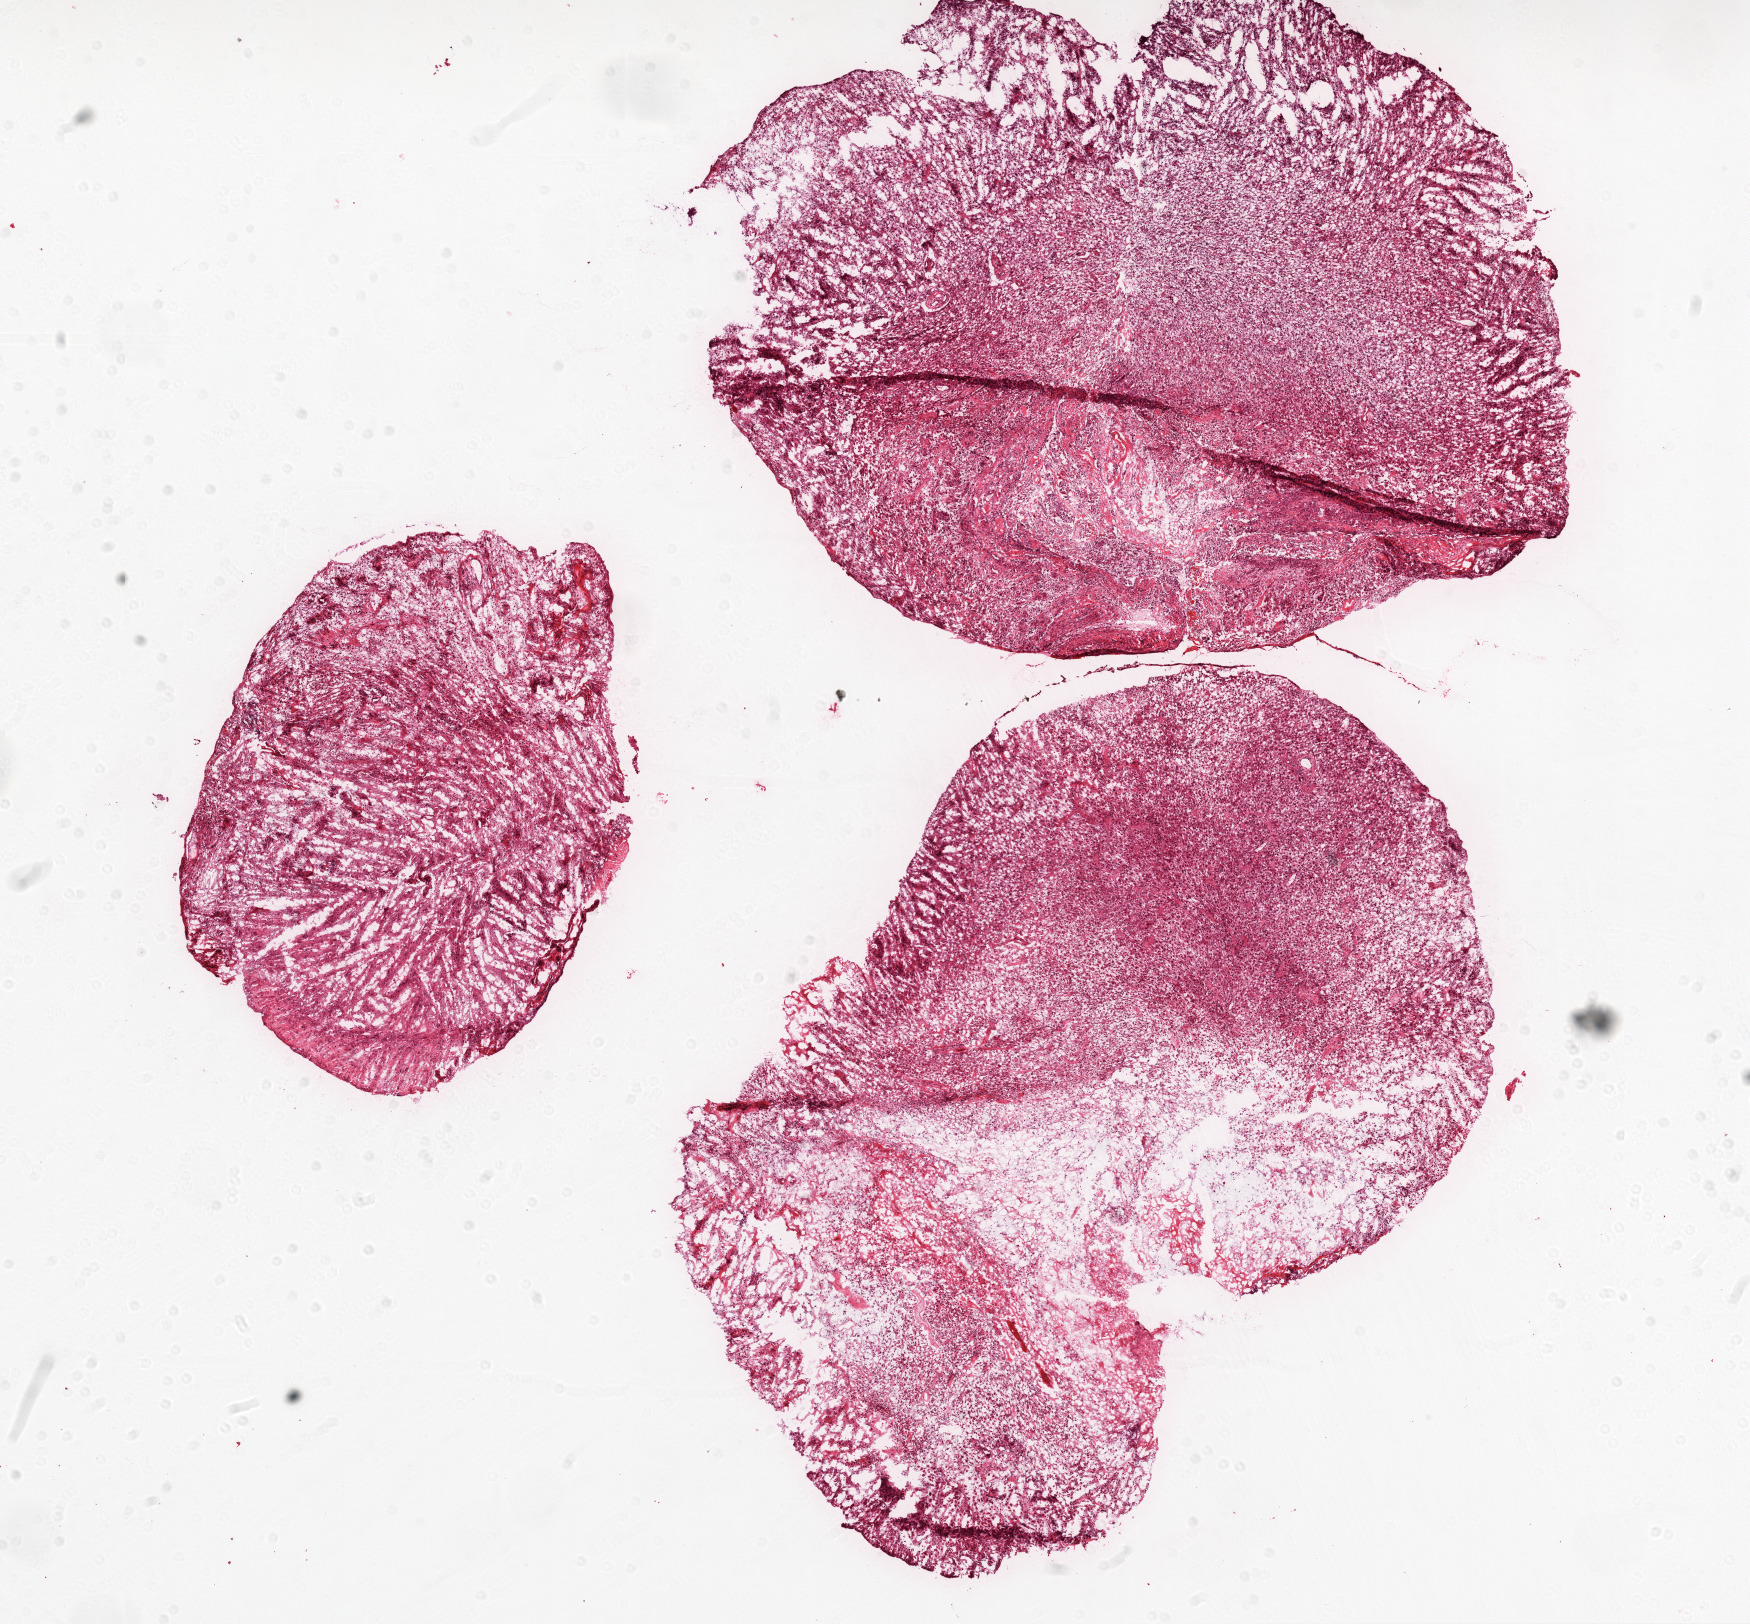
Whole-slide histology image, Hematoxylin and eosin (H&E) stained, shown as a low-resolution overview of the whole scanned area (about 14.0 x 13.0 mm, from a 20x scan); frozen section; sample: primary tumour, brain. Patient: male, age at initial diagnosis 57 years. Pathologist review of this section (percent, as recorded): tumour cells 95%, tumour nuclei 95%, normal cells 0%, stromal cells 5%, necrosis 0%.
* pathologic diagnosis: Glioblastoma